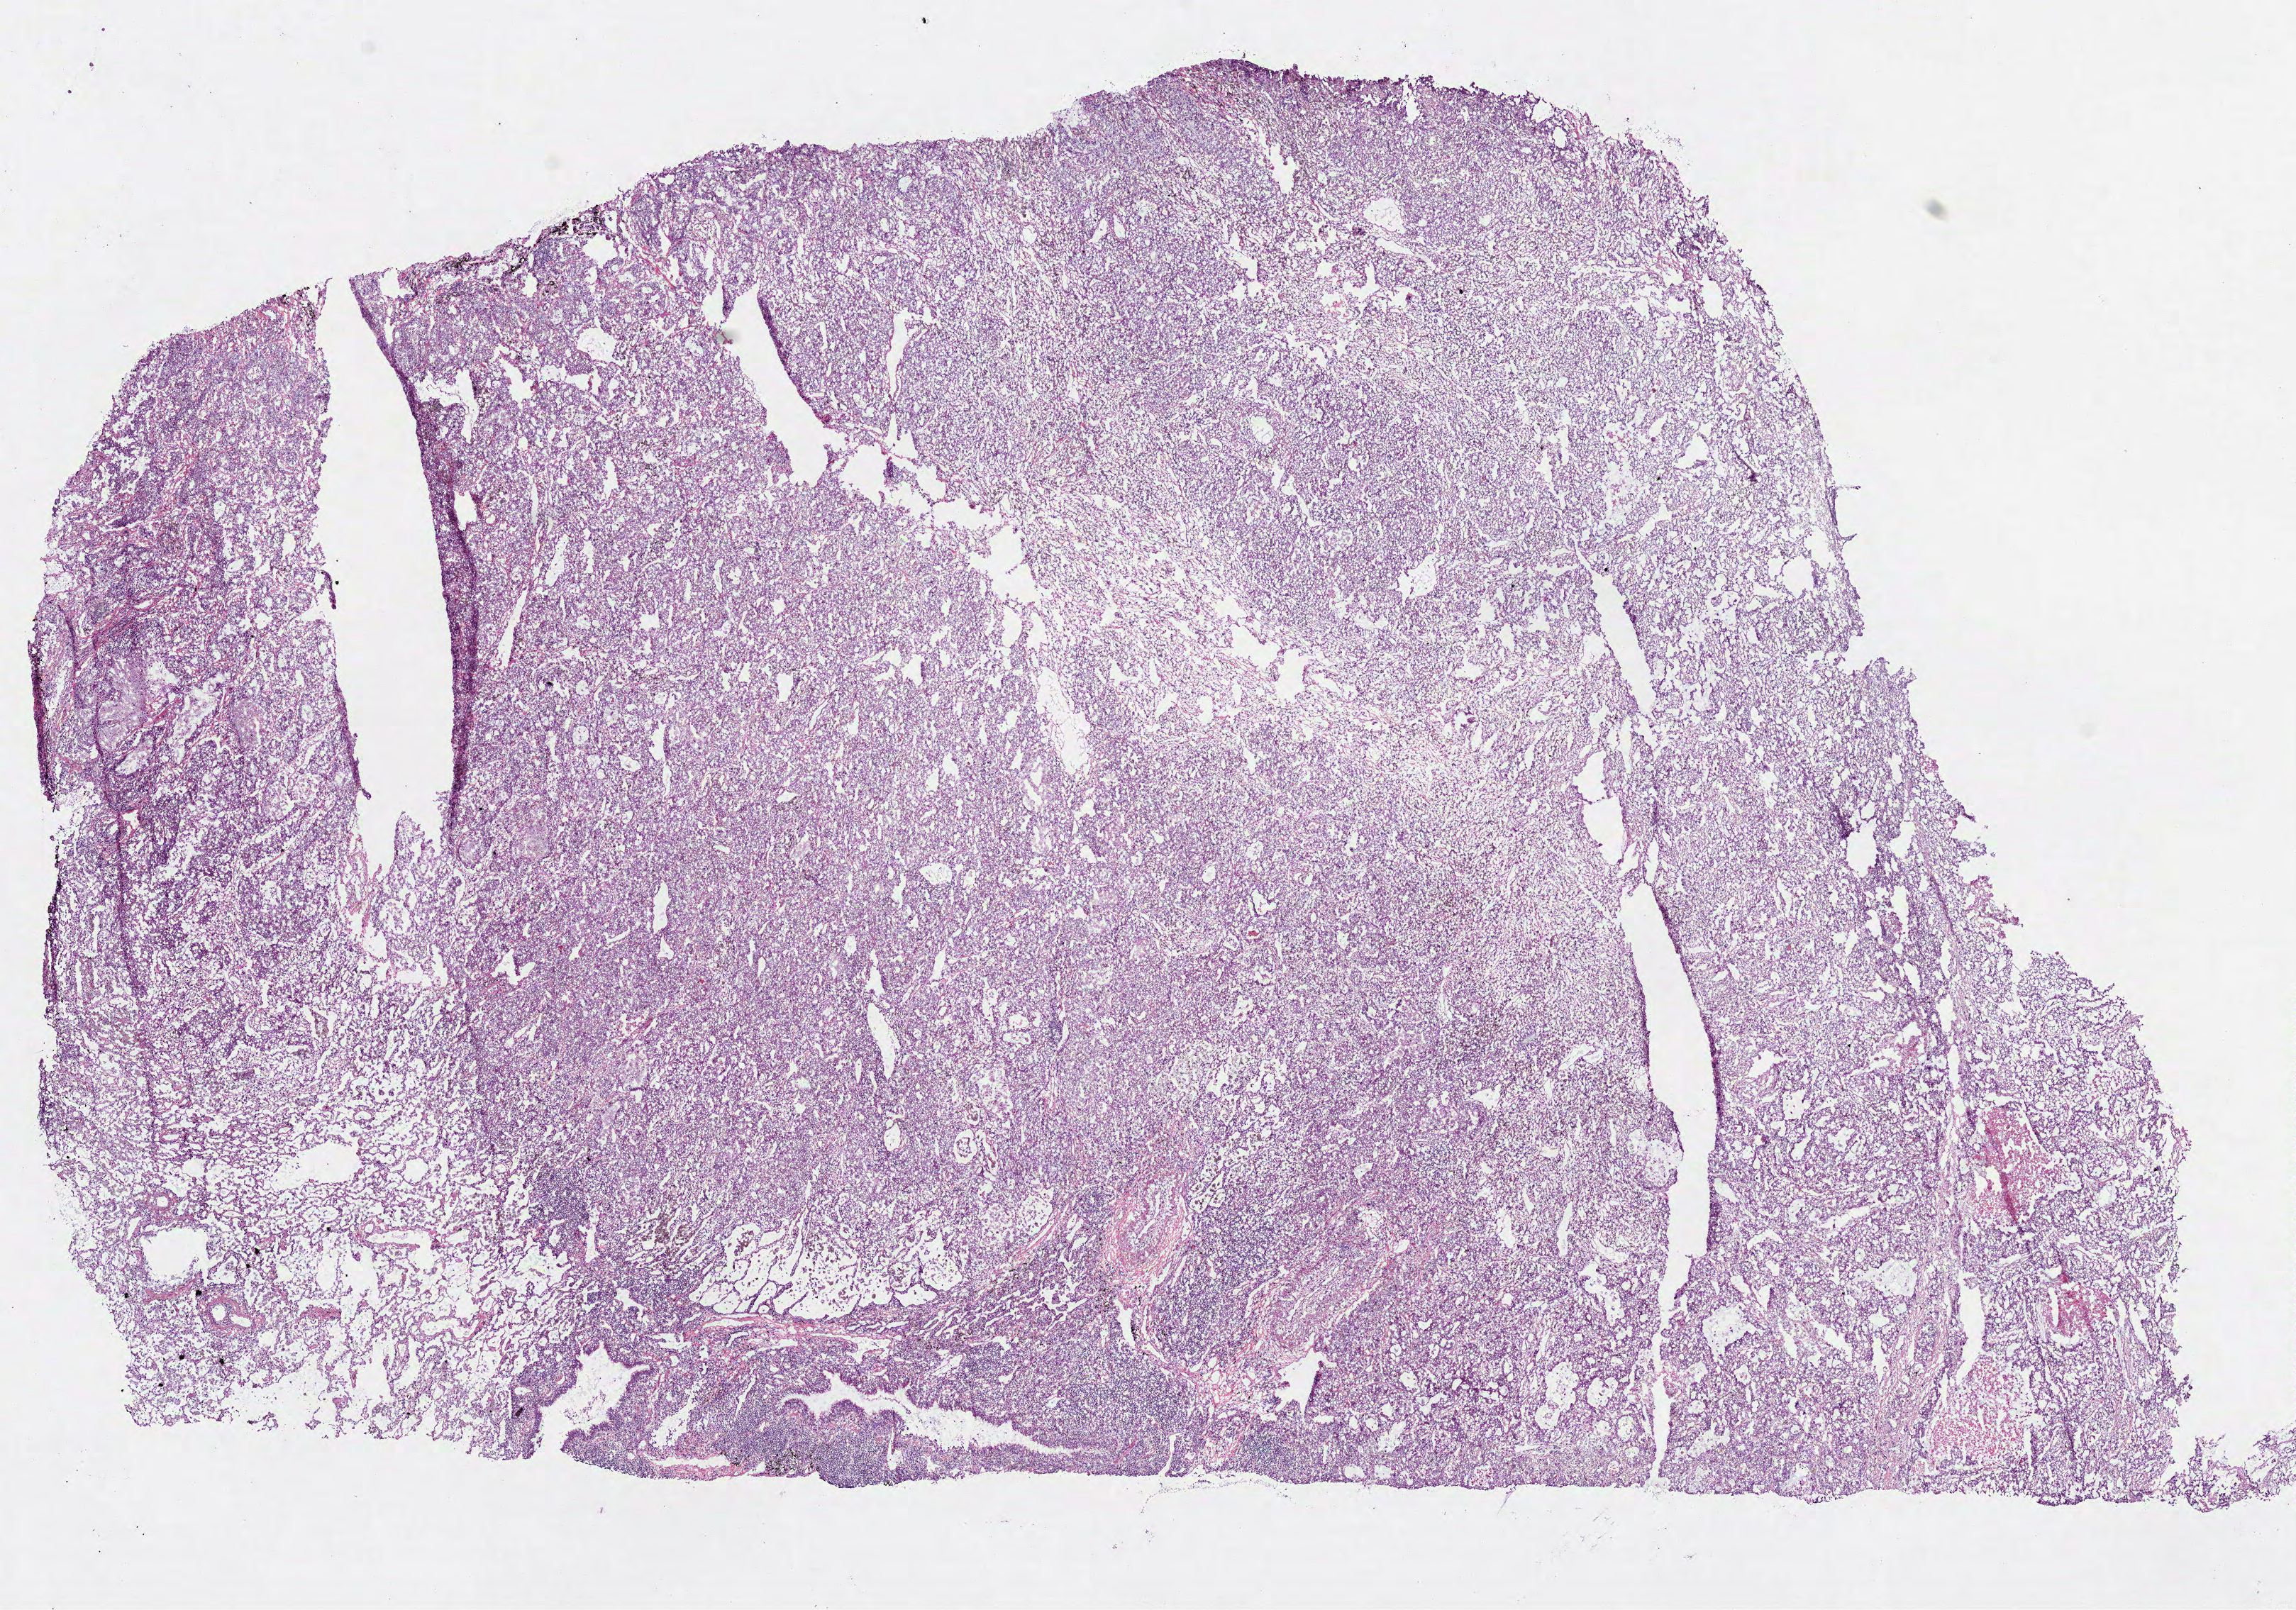
Digitized H&E tissue section (whole slide), whole scanned area (about 13.1 x 9.2 mm) shown as a low-resolution overview; frozen section from the top of the tissue portion; primary tumour sample from the lung. Male patient; age at initial diagnosis 47 years. Pathologist review of this section (percent, as recorded): tumour cells 80%, tumour nuclei 65%, normal cells 14%, stromal cells 0%, necrosis 6%. Inflammatory infiltration, as recorded: lymphocyte infiltration 10%, monocyte infiltration 5%, neutrophil infiltration 10%.
AJCC pathologic stage: IIIA. Pathologic diagnosis: Adenocarcinoma with mixed subtypes (lower lobe, lung).